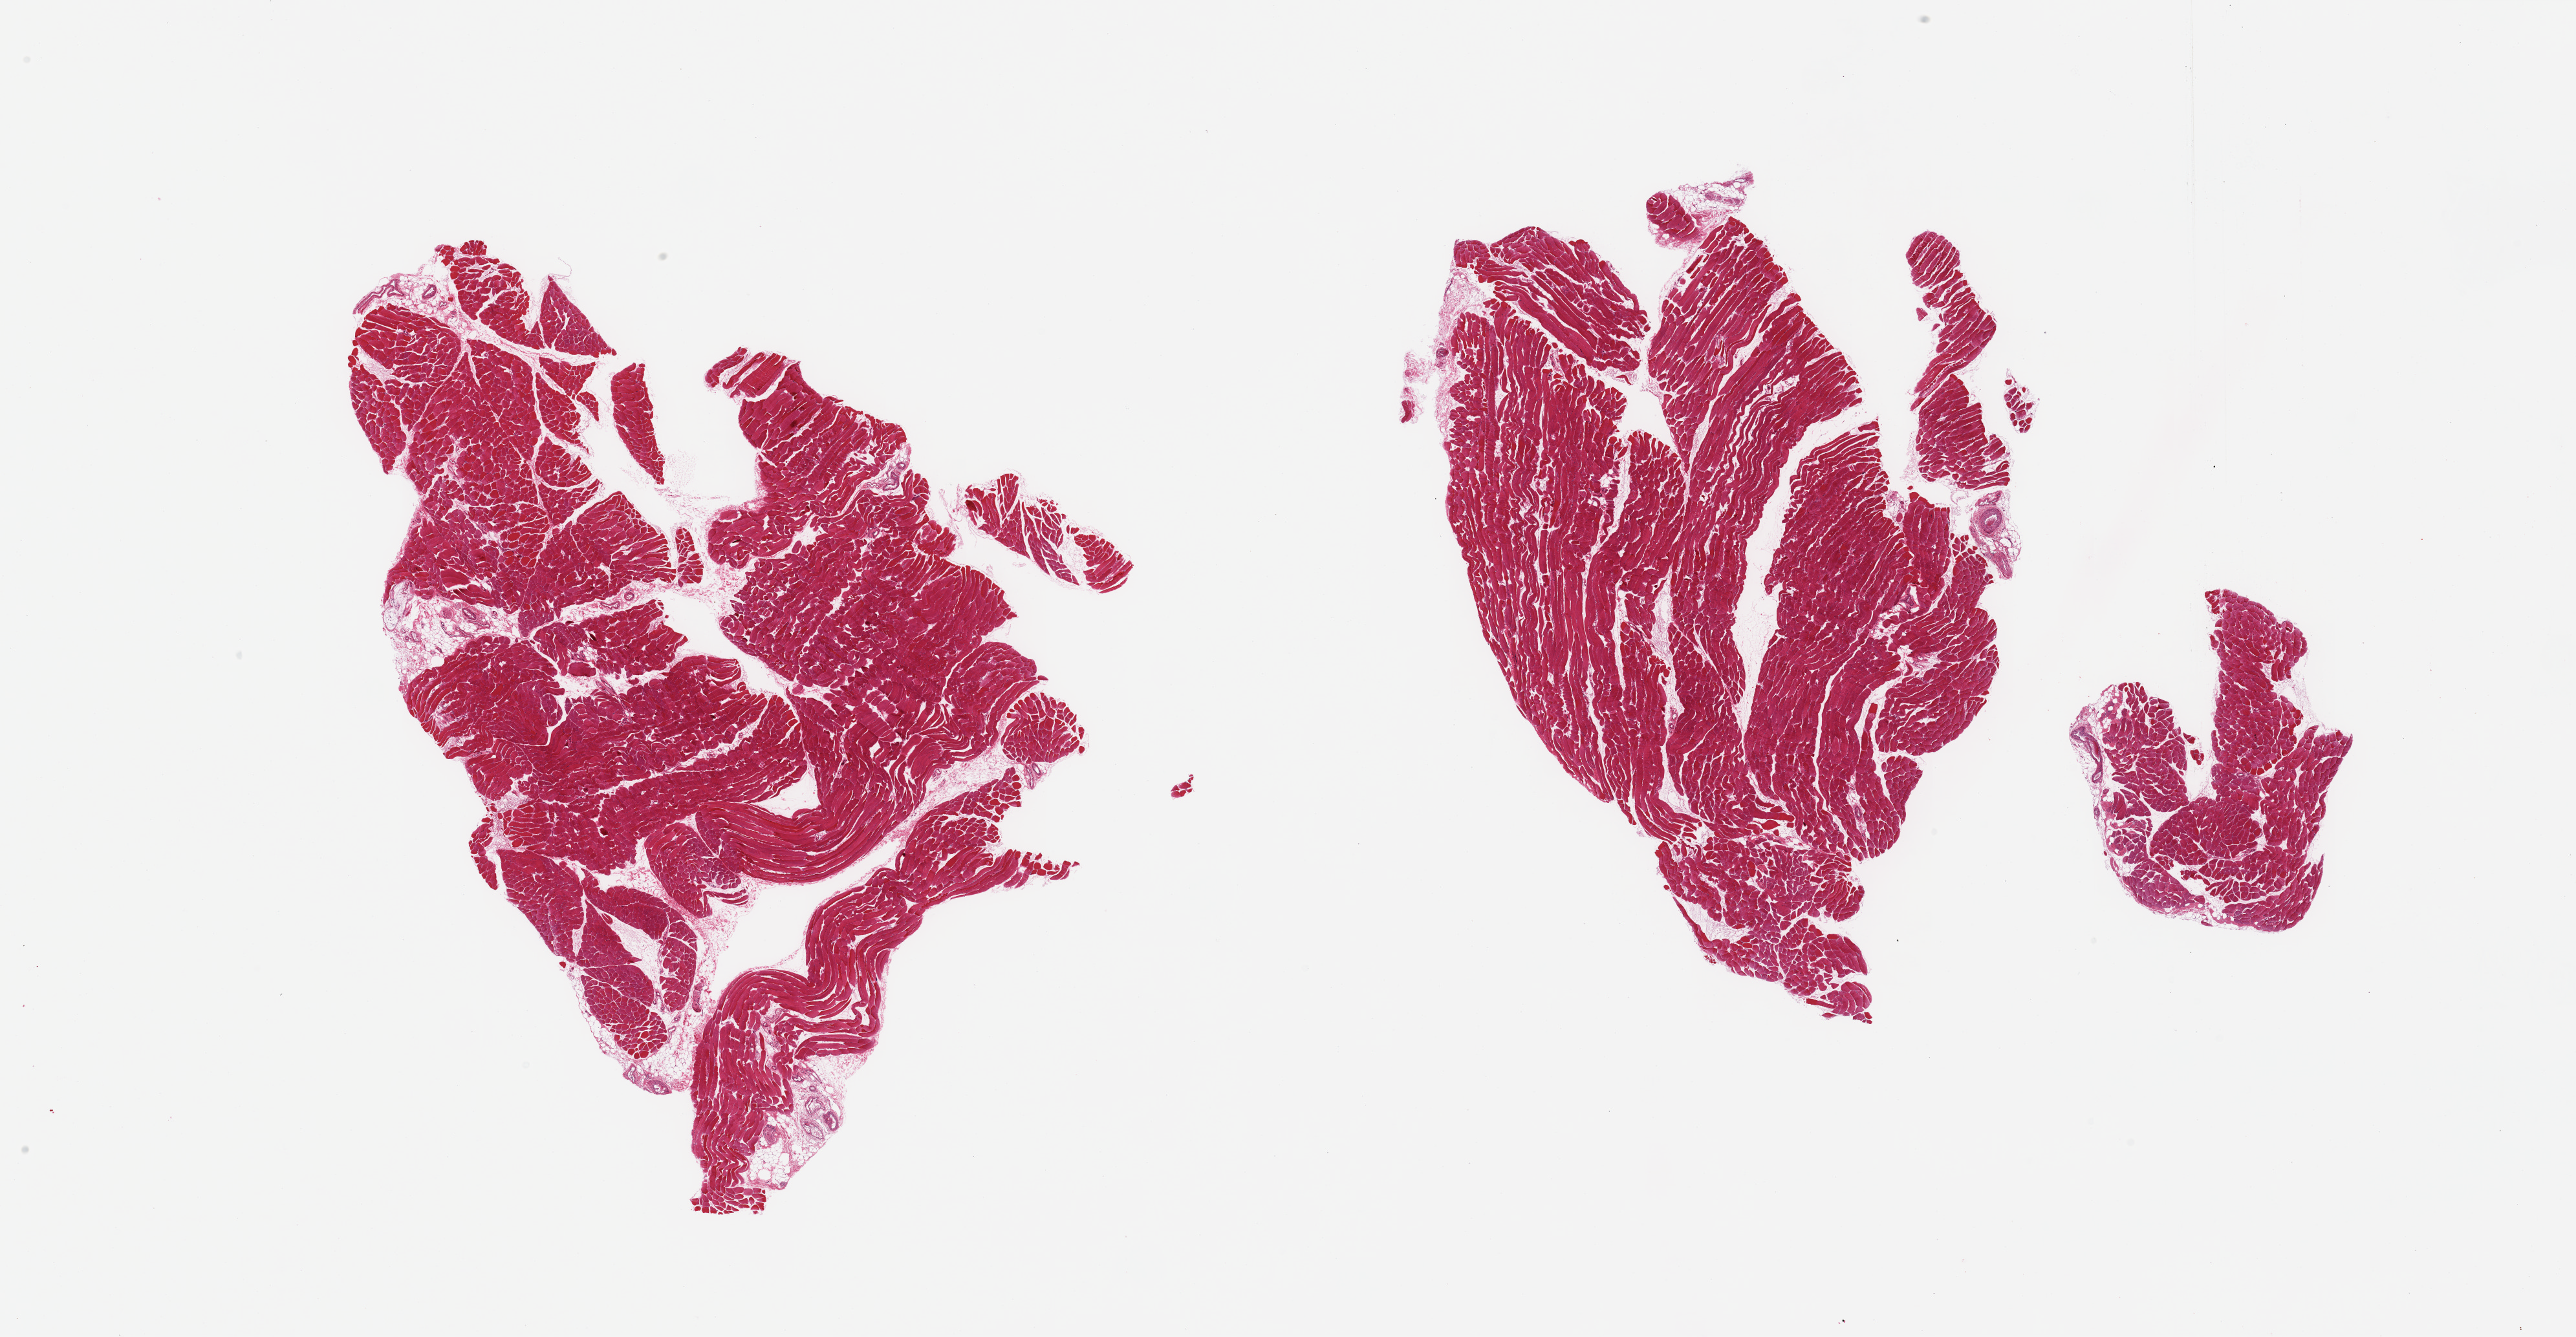
Digitized H&E-stained section, brightfield — low-resolution overview of the scanned area, about 31.5 x 16.4 mm (acquisition: 20x scan); PAXgene-fixed paraffin-embedded (PFPE) section; target tissue: skeletal muscle; donor tissue sample. Donor: male.
Review note (as recorded): 2 partly fragmented pieces; minimal fat content.